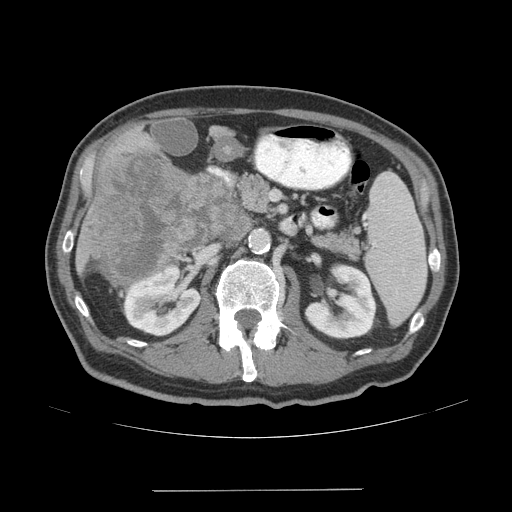
Contrast-enhanced abdominal CT (liver protocol), one axial slice. Slice 16 of 77 in the series (ordered by position). Reconstruction kernel STANDARD. 140 kVp. Soft-tissue window (W 400 / L 40 HU). 512 × 512 image matrix. From the clinical record (not read from this slice): diagnosis: hepatocellular carcinoma (patient treated with transarterial chemoembolisation; whether this scan precedes or follows treatment is not stated here); TNM stage (as recorded): Stage-IVA; Child-Pugh class: A; tumour differentiation: well differentiated; tumour nodularity: uninodular.
Outlined on this slice (semi-automatic segmentation, software-assisted and operator-edited):
- liver parenchyma outside the tumour (the mass and vessels are separate outlines, so this box may not span the whole liver): bounding box (x1, y1, x2, y2) in pixels: (76, 132, 162, 293)
- mass: (89, 146, 235, 288)